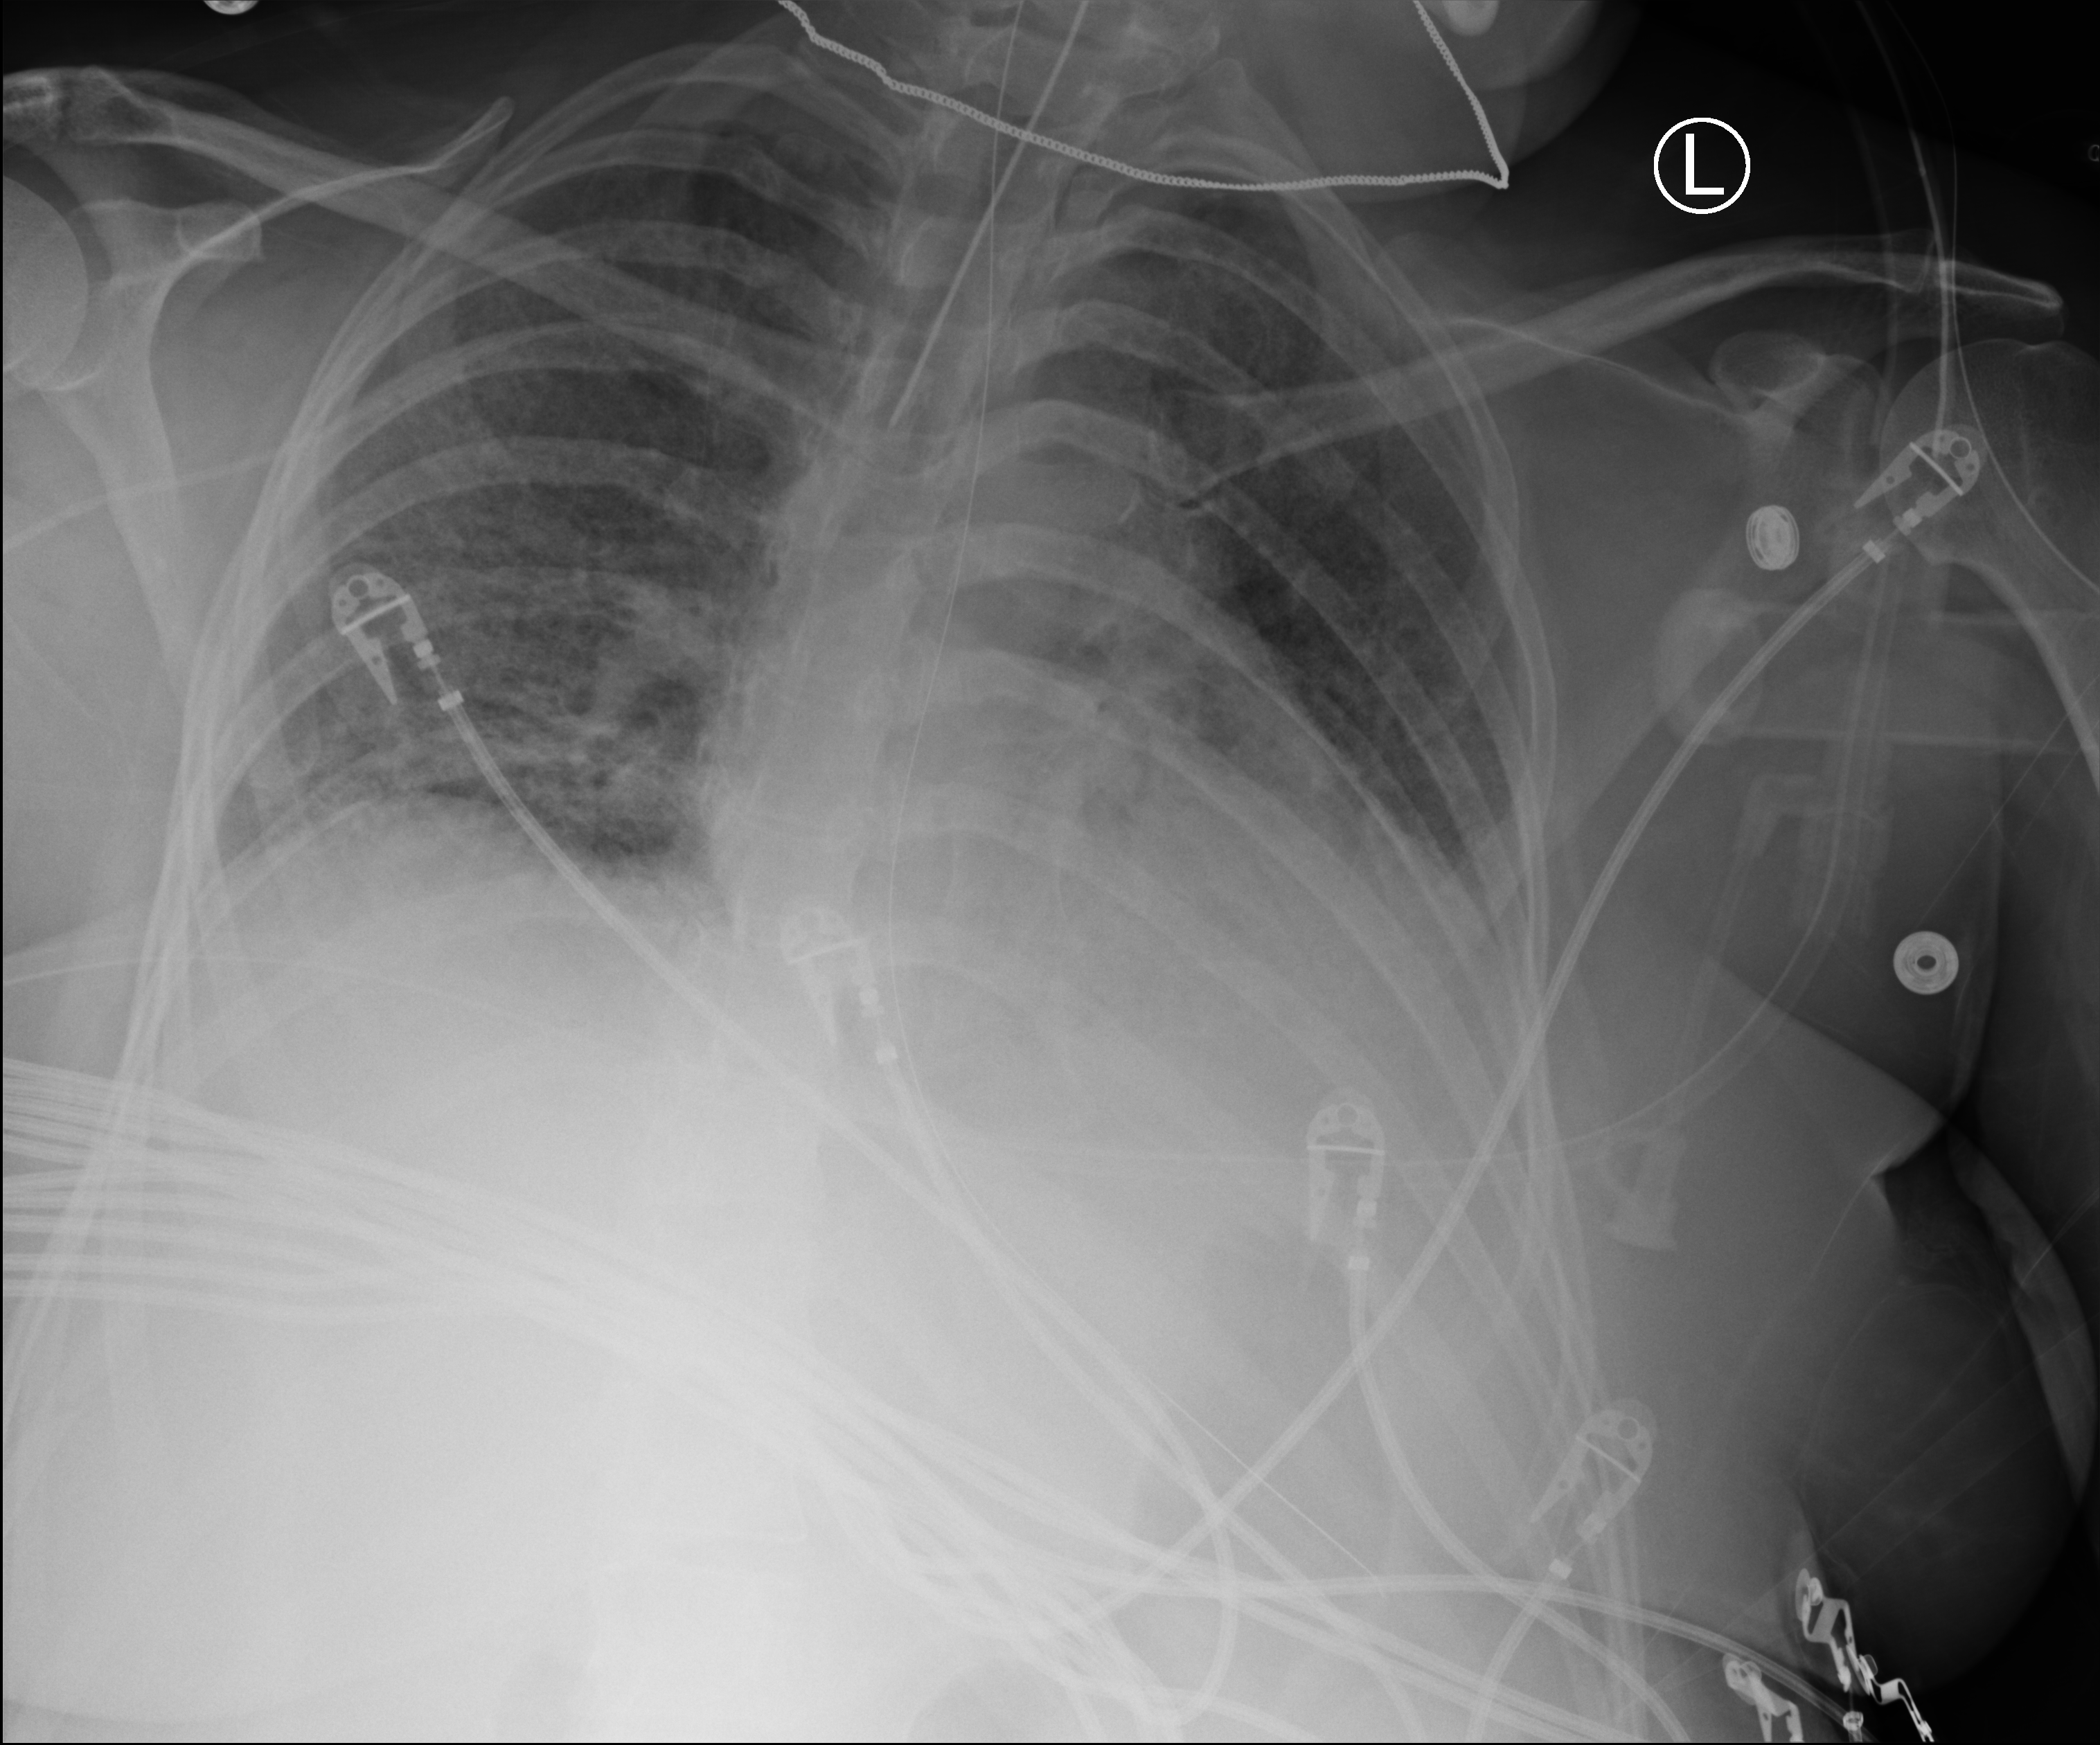
Bedside chest radiograph (computed radiography); anteroposterior (AP) projection. Patient hospitalised with COVID-19; female, aged 18–59 years.
From the hospital-stay record, not from the radiograph (when in the stay this image was taken is not recorded):
- admitted to intensive care during this hospital stay: yes
- other chronic lung disease (admission record): yes
- COPD (admission record): no